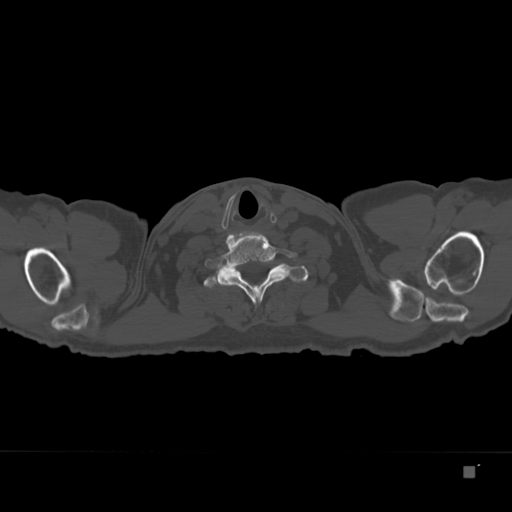
CT including the spine, one axial slice; position 325 of 332 along the scan axis; reconstruction kernel Br40s; 120 kVp; bone window (W 1800 / L 400 HU); 1.5 mm slice thickness; 512 × 512 image matrix, field of view 389 × 389 mm. Patient: male, 72 years. From the clinical record (not read from this slice): primary cancer: skeletal.
Annotated regions visible in this slice (semi-automatic segmentation, software-assisted and operator-edited):
- T1 vertebra: bounding box <204,263,309,289> (left, top, right, bottom; pixels)